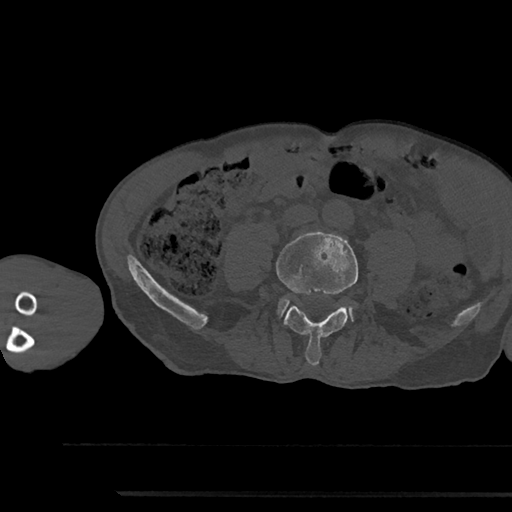
CT including the spine, one axial slice. Slice 396 of 797 in the series (ordered by position). Reconstruction kernel Br40s/3. Bone window (W 1800 / L 400 HU). 0.5 mm slice thickness. 512 × 512 image matrix, field of view 367 × 367 mm. Male patient, age 79 years. Case-level facts recorded for this patient, not image findings: primary cancer: prostate.
Outlined on this slice (semi-automatic segmentation, software-assisted and operator-edited):
- L4 vertebra: bounding box [x1, y1, x2, y2] px = [277, 232, 358, 366]
- L5 vertebra: [279, 299, 352, 317]